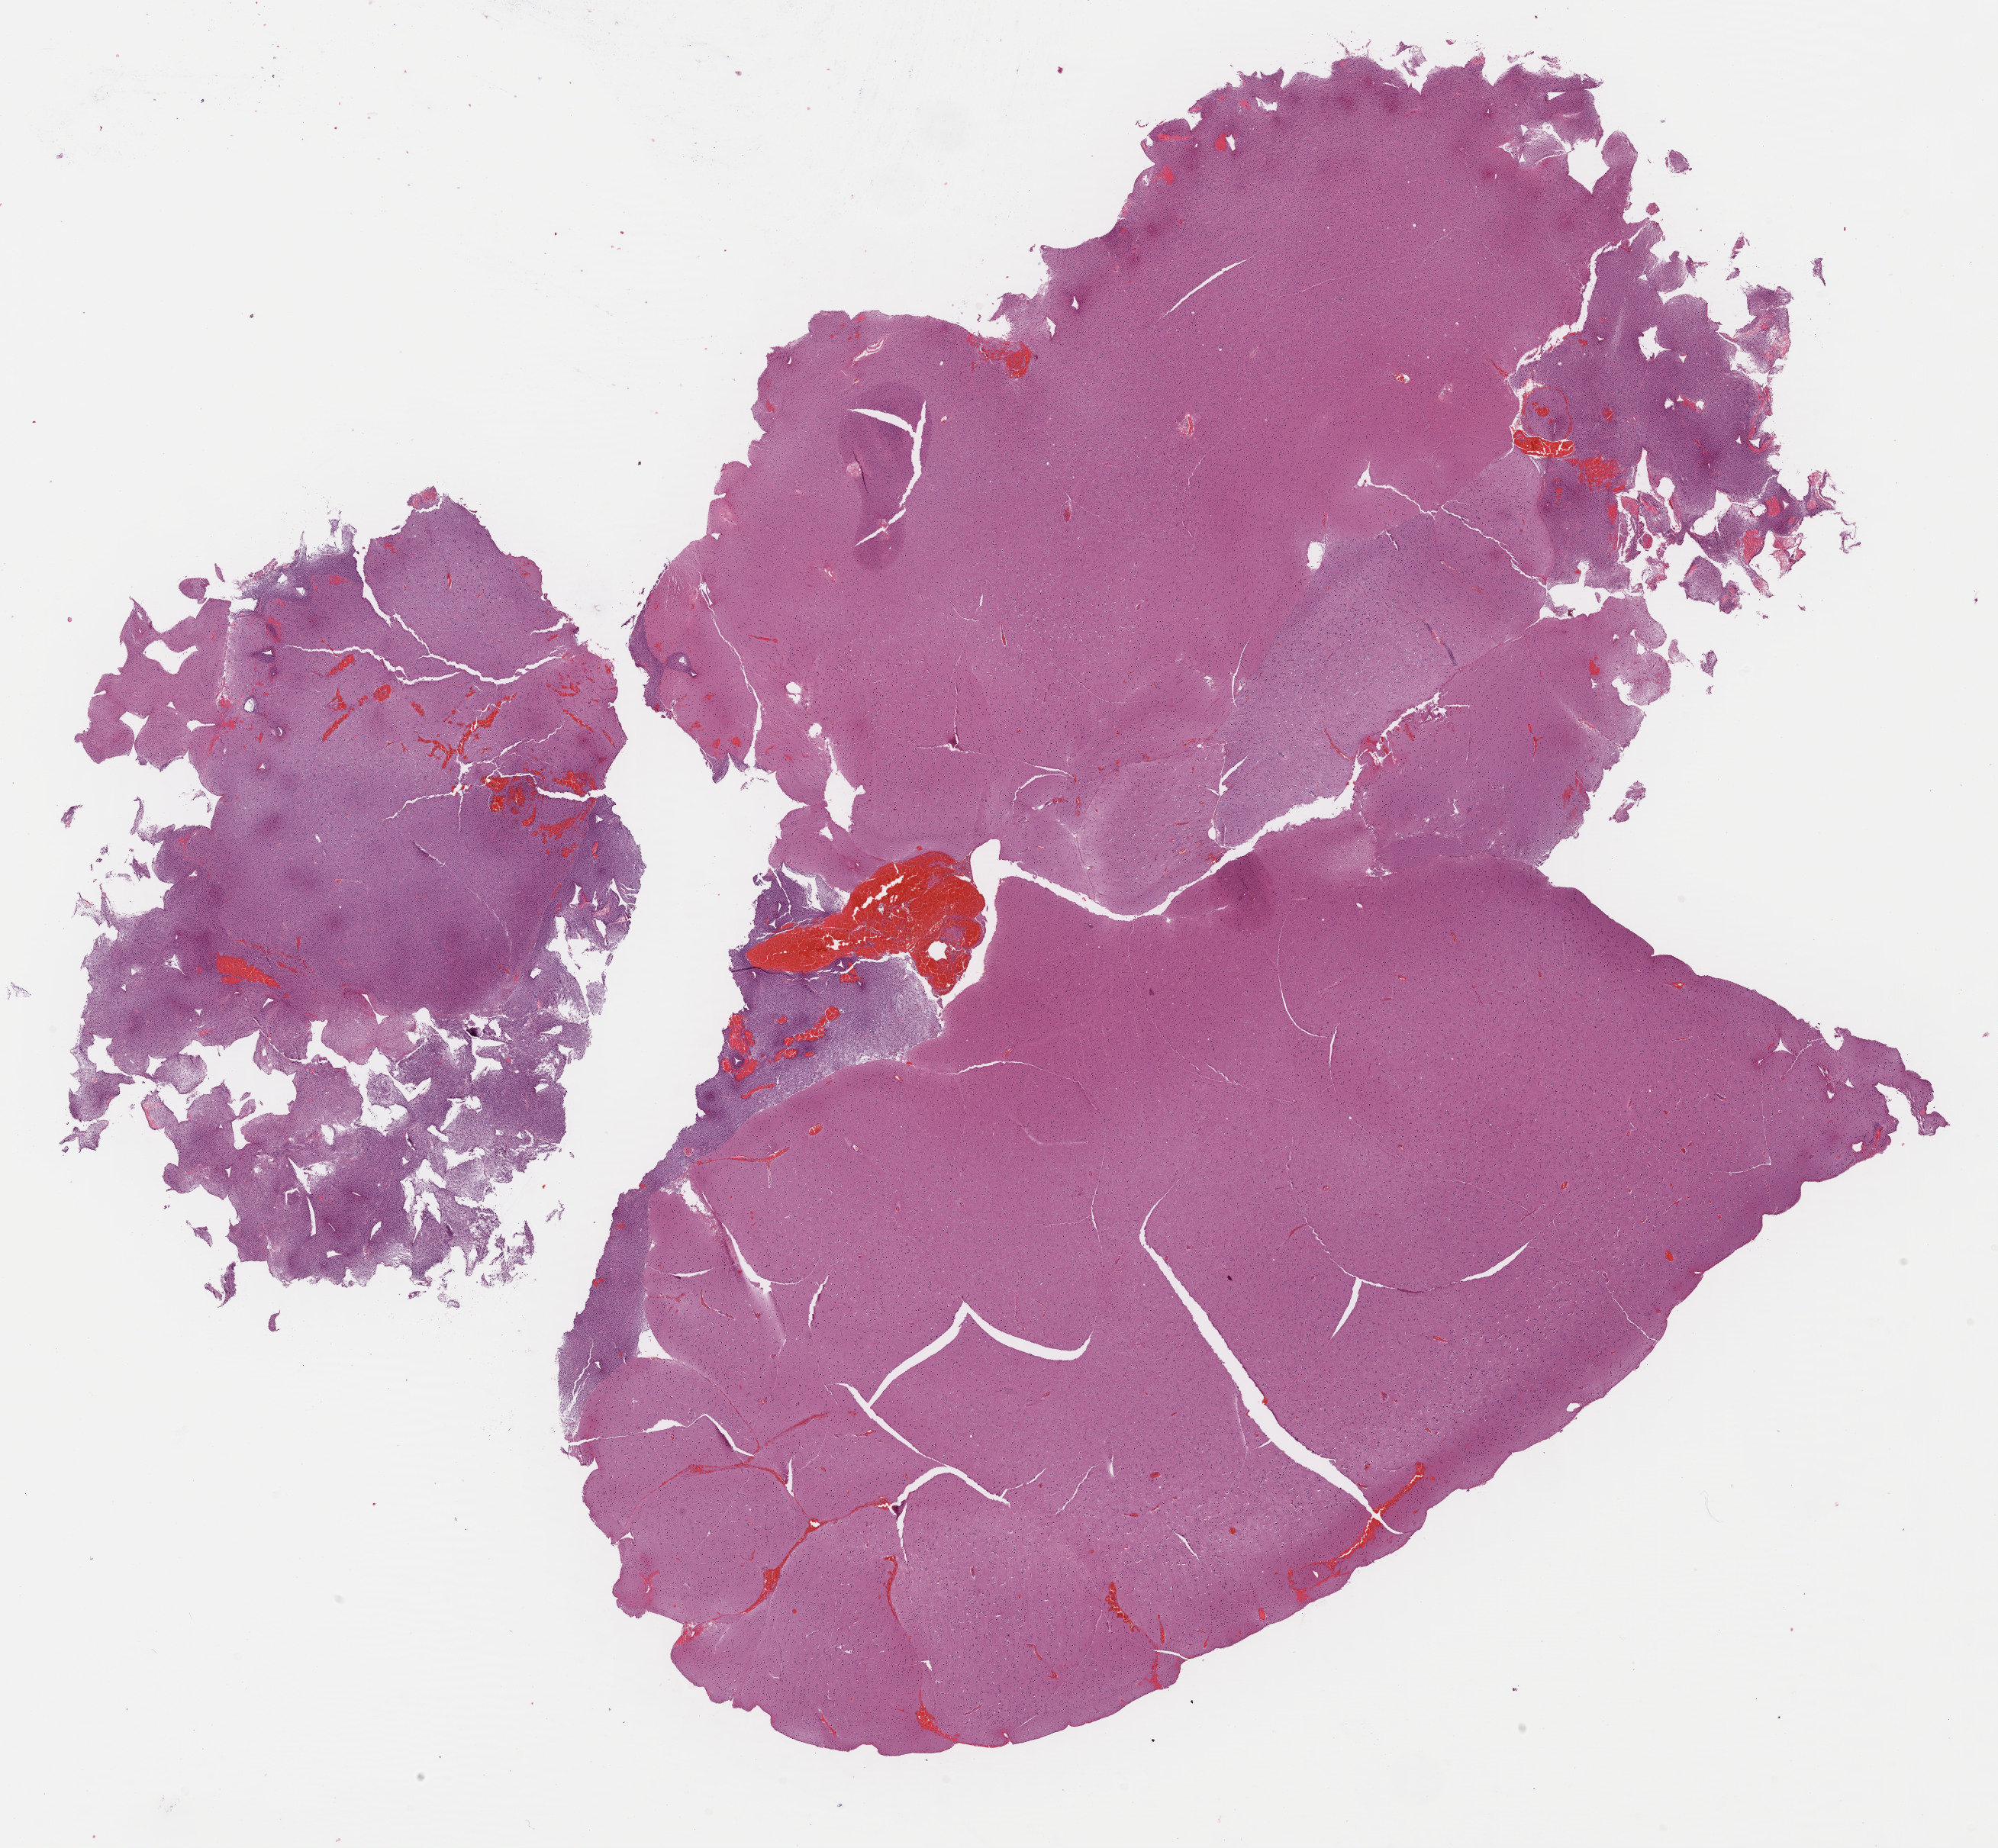
Digitized Hematoxylin and eosin (H&E) stained tissue section (whole slide) — whole scanned area (about 20.6 x 19.0 mm, slide scanned at 40x) shown as a low-resolution overview. Formalin-fixed paraffin-embedded (FFPE) diagnostic section. Sample: primary tumour, brain. Male patient; age at initial diagnosis 30 years. Histologic grade: G2 (moderately differentiated).
Laterality: right. Diagnosis: Mixed glioma (cerebrum).